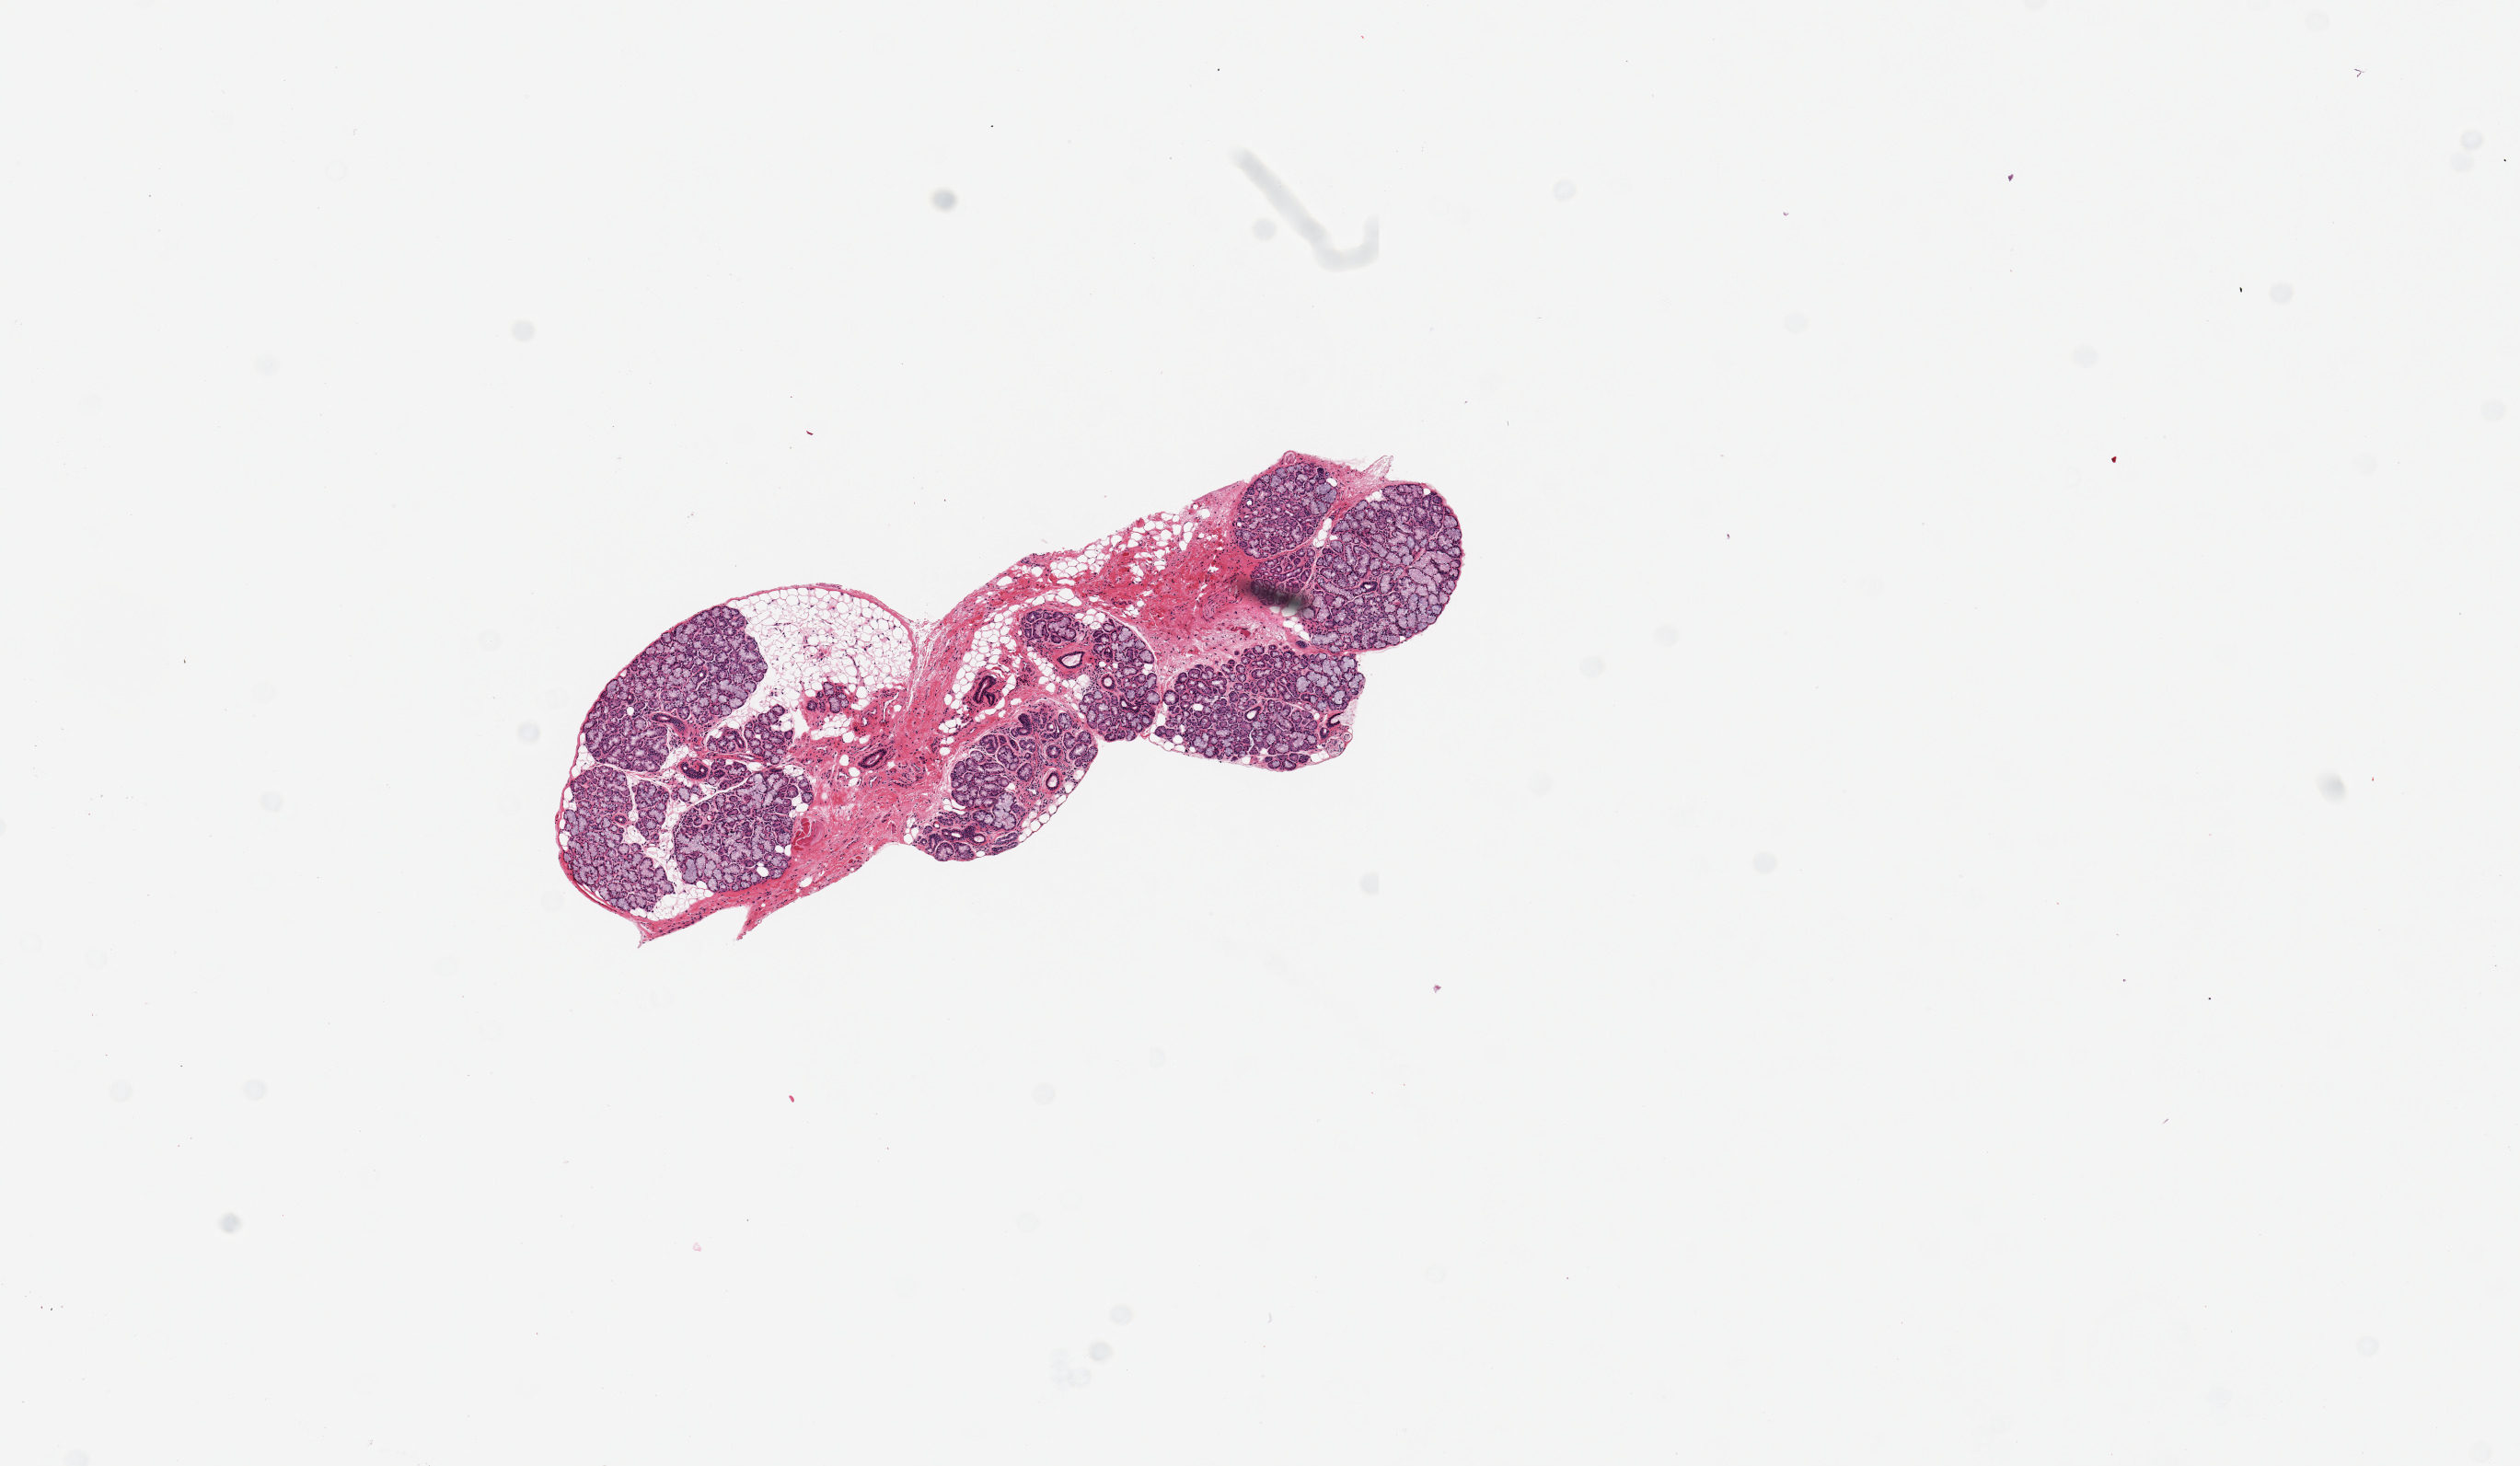
Digitized H&E-stained section — shown as a low-resolution overview of the whole scanned area (about 10.8 x 6.3 mm, slide scanned at 20x); PAXgene-fixed paraffin-embedded (PFPE) section; target tissue: minor salivary gland; donor tissue sample. Female donor.
Reviewer comment on this tissue sample: 1 piece, 4x1.5mm; good specmen; 40% is fat/fibrous interstitial tissue.